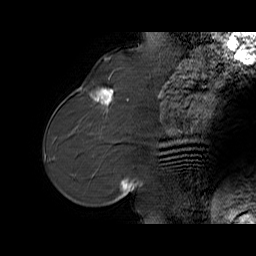
Breast MRI (dynamic contrast-enhanced), one sagittal slice; position 23 of 65 along the scan axis; dynamic contrast-enhanced series, time point 2 of 6 at this slice position (early post-contrast); 1.5 T; TE 5.7 ms, TR 32.9 ms; 4 mm slice thickness; 256 × 256 image matrix, field of view 230 × 230 mm. Female patient. Case-level facts recorded for this patient, not image findings: setting: breast cancer imaged before/during neoadjuvant chemotherapy; receptor status: HER2-positive.
Structures marked on this image (semi-automatically segmented with operator editing):
- analysis volume of interest (the breast-tissue region the enhancement analysis was run in; not a lesion): bounding box [x1, y1, x2, y2] px = [76, 77, 125, 128]
- tumour enhancement mask (voxels above the 100 % enhancement threshold inside the analysis volume of interest): [90, 87, 113, 105]